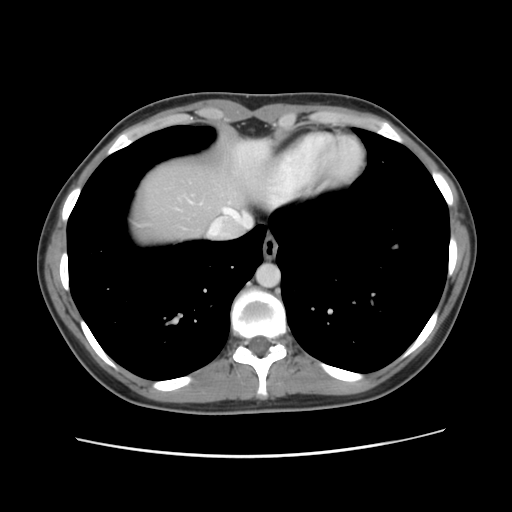
Contrast-enhanced abdominal CT, one axial slice. Slice 114 of 134 in the series (ordered by position). 120 kVp. Intravenous contrast given. Soft-tissue window (W 400 / L 40 HU). 512 × 512 image matrix, field of view 339 × 339 mm. Female patient, age 33 years. From the clinical record (not read from this slice): diagnosis: colorectal cancer liver metastases, imaged before liver resection; multiple liver metastases: yes; largest metastasis: 4.5 cm.
Structures marked on this image (manually delineated by an expert):
- hepatic veins: bounding box (x1, y1, x2, y2) in pixels: (224, 208, 250, 225)
- liver: (128, 151, 265, 246)
- planned liver remnant (the part of the liver to remain after resection): (128, 151, 259, 246)